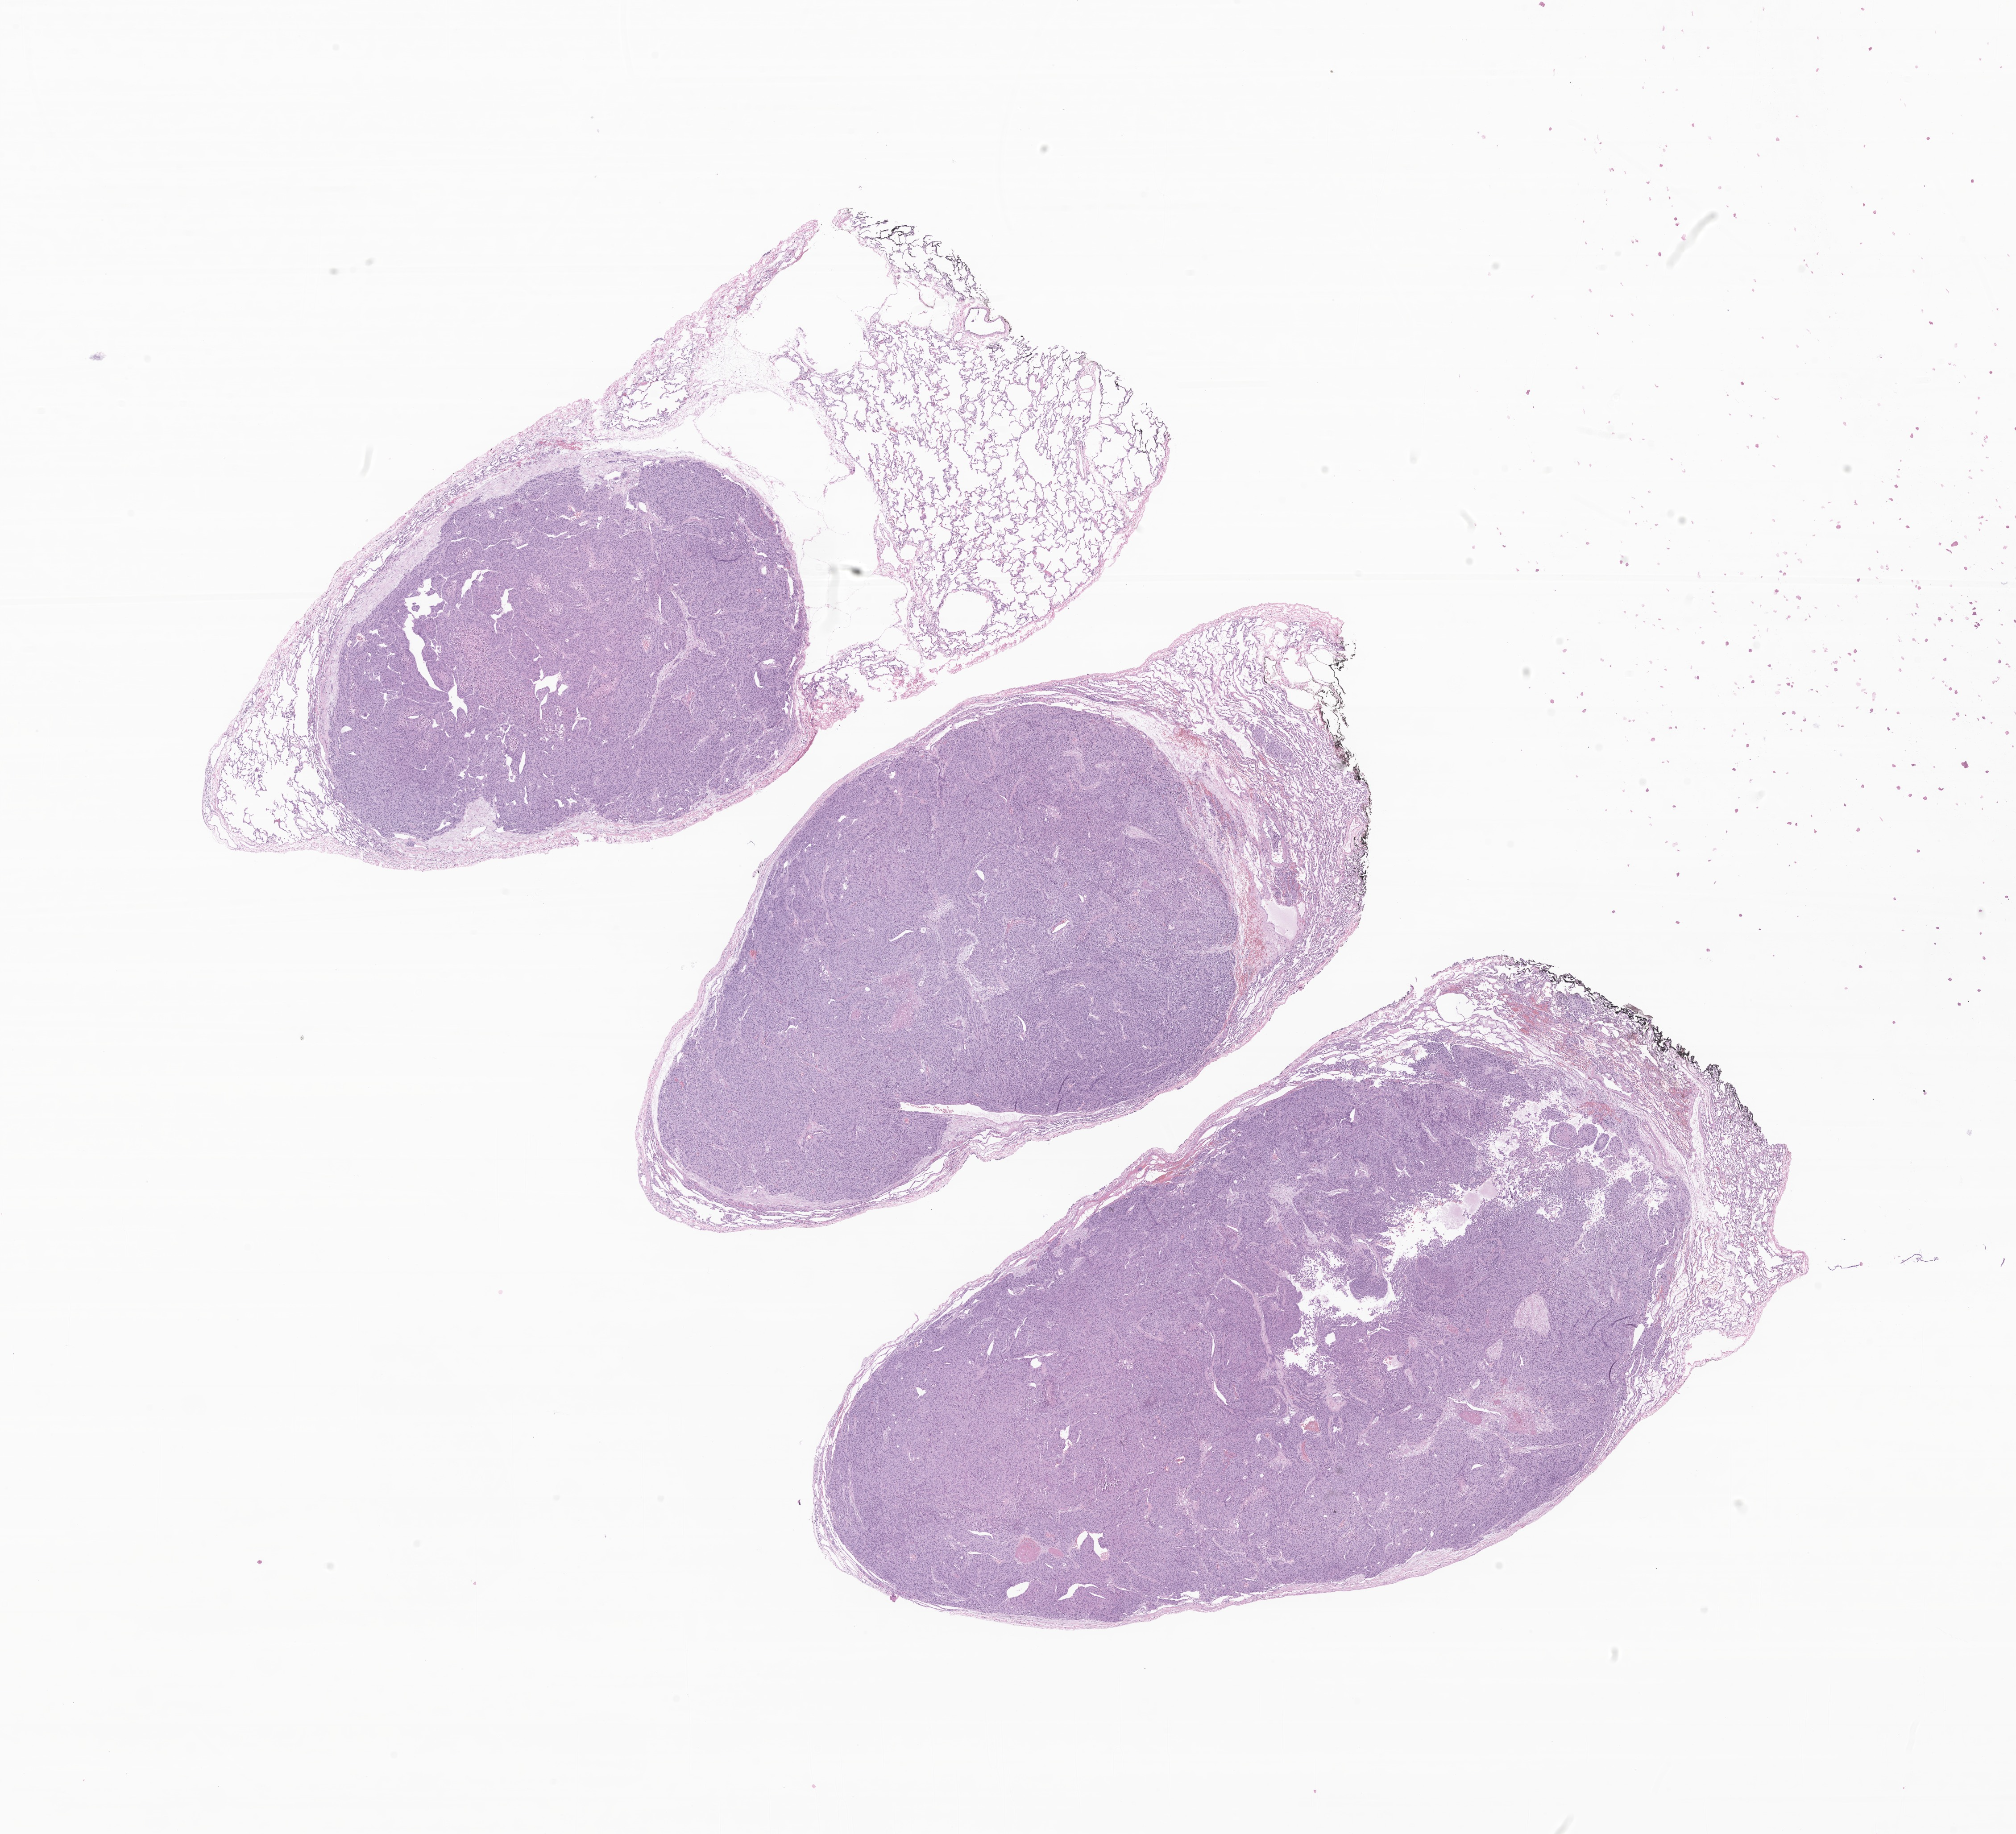
Whole-slide image, haematoxylin and eosin stain of tumor tissue from the adrenal gland, shown as a low-resolution overview of the whole scanned area (about 19.0 x 17.3 mm); FFPE section. Male patient, age 94 months (7 years 10 months).
Diagnosis: Adrenal cortical carcinoma.